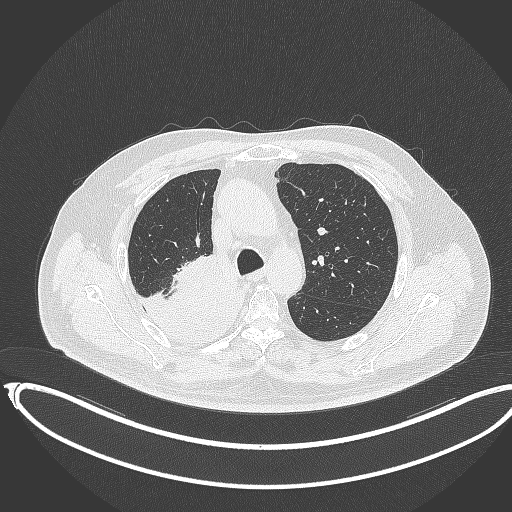
Chest CT, one axial slice; position 254 of 403 along the scan axis; reconstruction kernel B70f; 120 kVp; lung window (W 1500 / L -600 HU); 1 mm slice thickness; 512 × 512 image matrix. Patient: male, 68 years. From the clinical record (not read from this slice): clinical TNM (as recorded): T2a N0 M0.
Structures marked on this image (rectangle marked by the reading radiologist):
- lung tumour (recorded histology: adenocarcinoma): box from (x=130, y=252) to (x=241, y=349) px